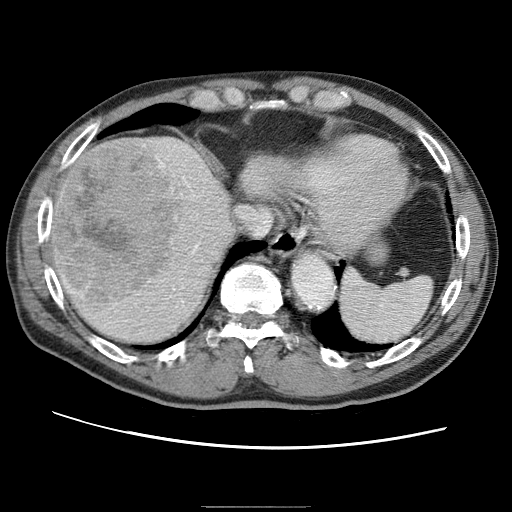
Contrast-enhanced abdominal CT (liver protocol), one axial slice. Slice 55 of 75 in the series (ordered by position). 120 kVp. One of 2 acquisitions stored at this slice position. Soft-tissue window (W 400 / L 40 HU). 2.5 mm slice thickness. 512 × 512 image matrix, field of view 360 × 360 mm. From the clinical record (not read from this slice): diagnosis: hepatocellular carcinoma (patient treated with transarterial chemoembolisation; whether this scan precedes or follows treatment is not stated here); TNM stage (as recorded): Stage-II; Child-Pugh class: A; tumour differentiation: well differentiated; tumour nodularity: multinodular.
Structures marked on this image (semi-automatic segmentation, software-assisted and operator-edited):
- abdominal aorta: box from (x=292, y=253) to (x=333, y=308) px
- liver parenchyma outside the tumour (the mass and vessels are separate outlines, so this box may not span the whole liver): (x=49, y=134)–(x=292, y=346)
- mass: (x=55, y=140)–(x=185, y=303)
- liver vessels: (x=53, y=179)–(x=201, y=305)